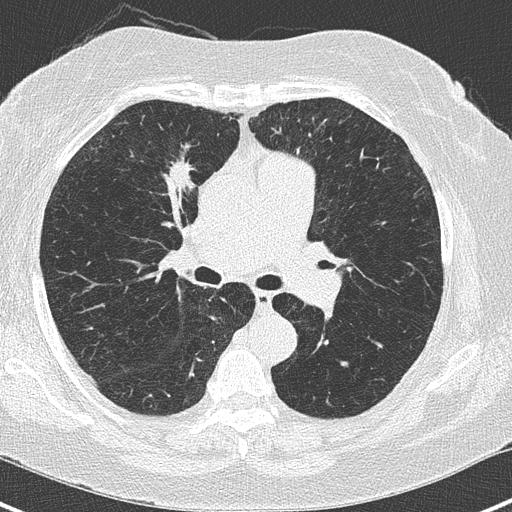
Chest CT (low-dose screening protocol), one axial image. Third screening round (two years after baseline). Lung window (W 1500 / L -600 HU). 2 mm slice thickness. Lung (sharp) reconstruction kernel (B50f). 512 × 512 image matrix, field of view 303 × 303 mm. Female, age 62 years at enrolment. Current smoker at enrolment.
Expert reader's lesion annotation, bounding box <146,149,211,208> (left, top, right, bottom; pixels). The screening reader recorded 4 non-calcified nodules or masses ≥4 mm on this exam (right upper lobe, left lower lobe, left lower lobe); which of them this box marks is not recorded. Later outcome: lung cancer diagnosed 41 days after this screen — adenocarcinoma, NOS, right upper lobe, moderately differentiated (G2), stage IA (AJCC 6th edition), 15 mm at pathology.